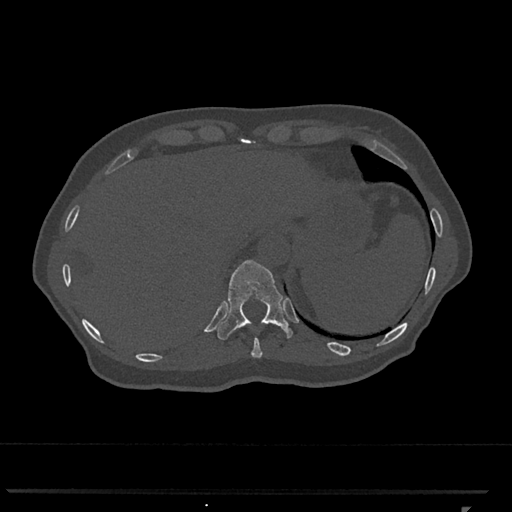
CT including the spine, one axial slice. Position 532 of 793 along the scan axis. Reconstruction kernel Br40s/3. 120 kVp. Bone window (W 1800 / L 400 HU). 0.5 mm slice thickness. 512 × 512 image matrix, field of view 380 × 380 mm. Female patient, age 62 years. Case-level facts recorded for this patient, not image findings: primary cancer: renal.
Outlined on this slice (semi-automatic segmentation, software-assisted and operator-edited):
- T10 vertebra: bounding box <251,338,263,358> (left, top, right, bottom; pixels)
- T11 vertebra: <217,260,293,340>